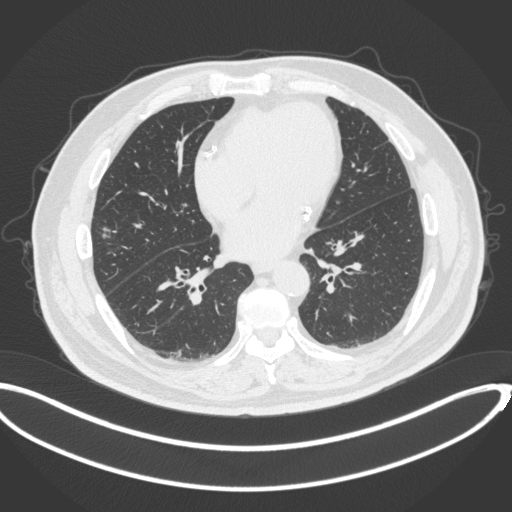
Chest CT, one axial slice; lung window (W 1500 / L -600 HU); 1 mm slice thickness; 512 × 512 image matrix. Patient: male, 68 years. Case-level facts recorded for this patient, not image findings: clinical TNM (as recorded): T1c N0 M0.
Structures marked on this image (rectangle marked by the reading radiologist):
- lung tumour (recorded histology: adenocarcinoma): bounding box [x1, y1, x2, y2] px = [100, 226, 112, 241]